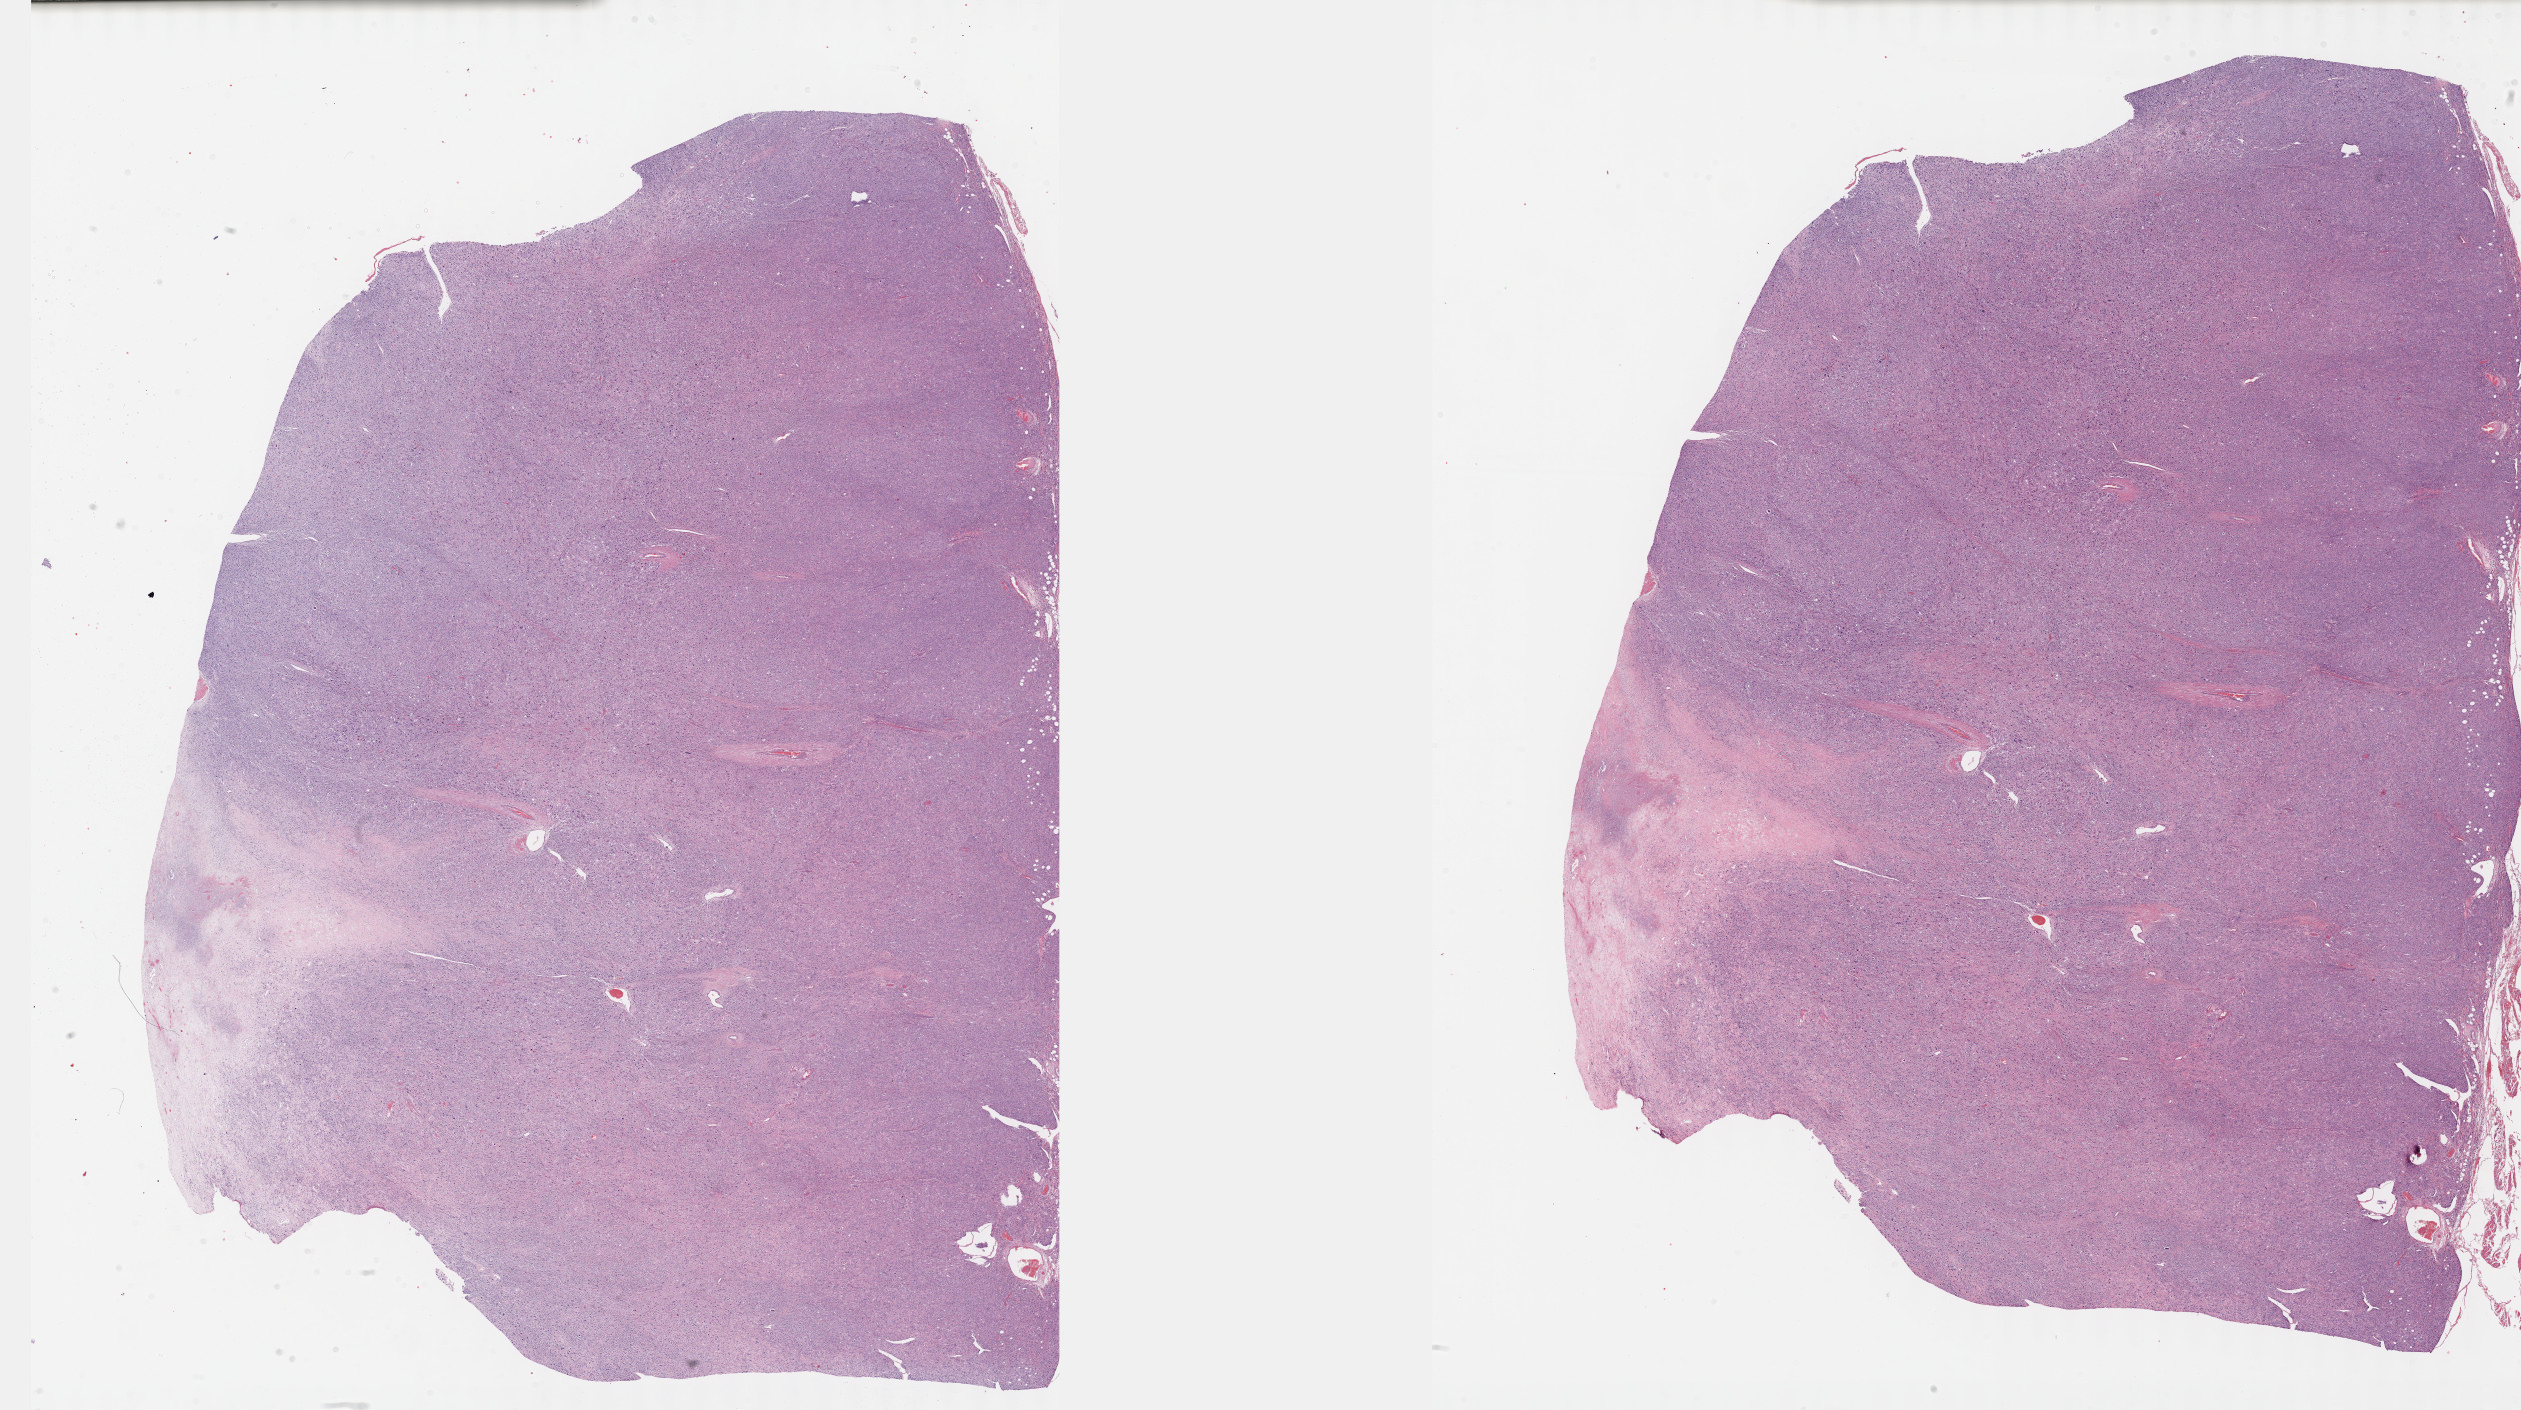
Whole-slide histology image, Hematoxylin and eosin (H&E) stained — a low-resolution overview of the entire scanned area, about 40.7 x 22.8 mm; formalin-fixed paraffin-embedded (FFPE) diagnostic section; connective, subcutaneous and other soft tissues, primary tumour sample. Male, age 76 years at initial diagnosis.
Diagnosis: Undifferentiated sarcoma (connective, subcutaneous and other soft tissues, NOS).